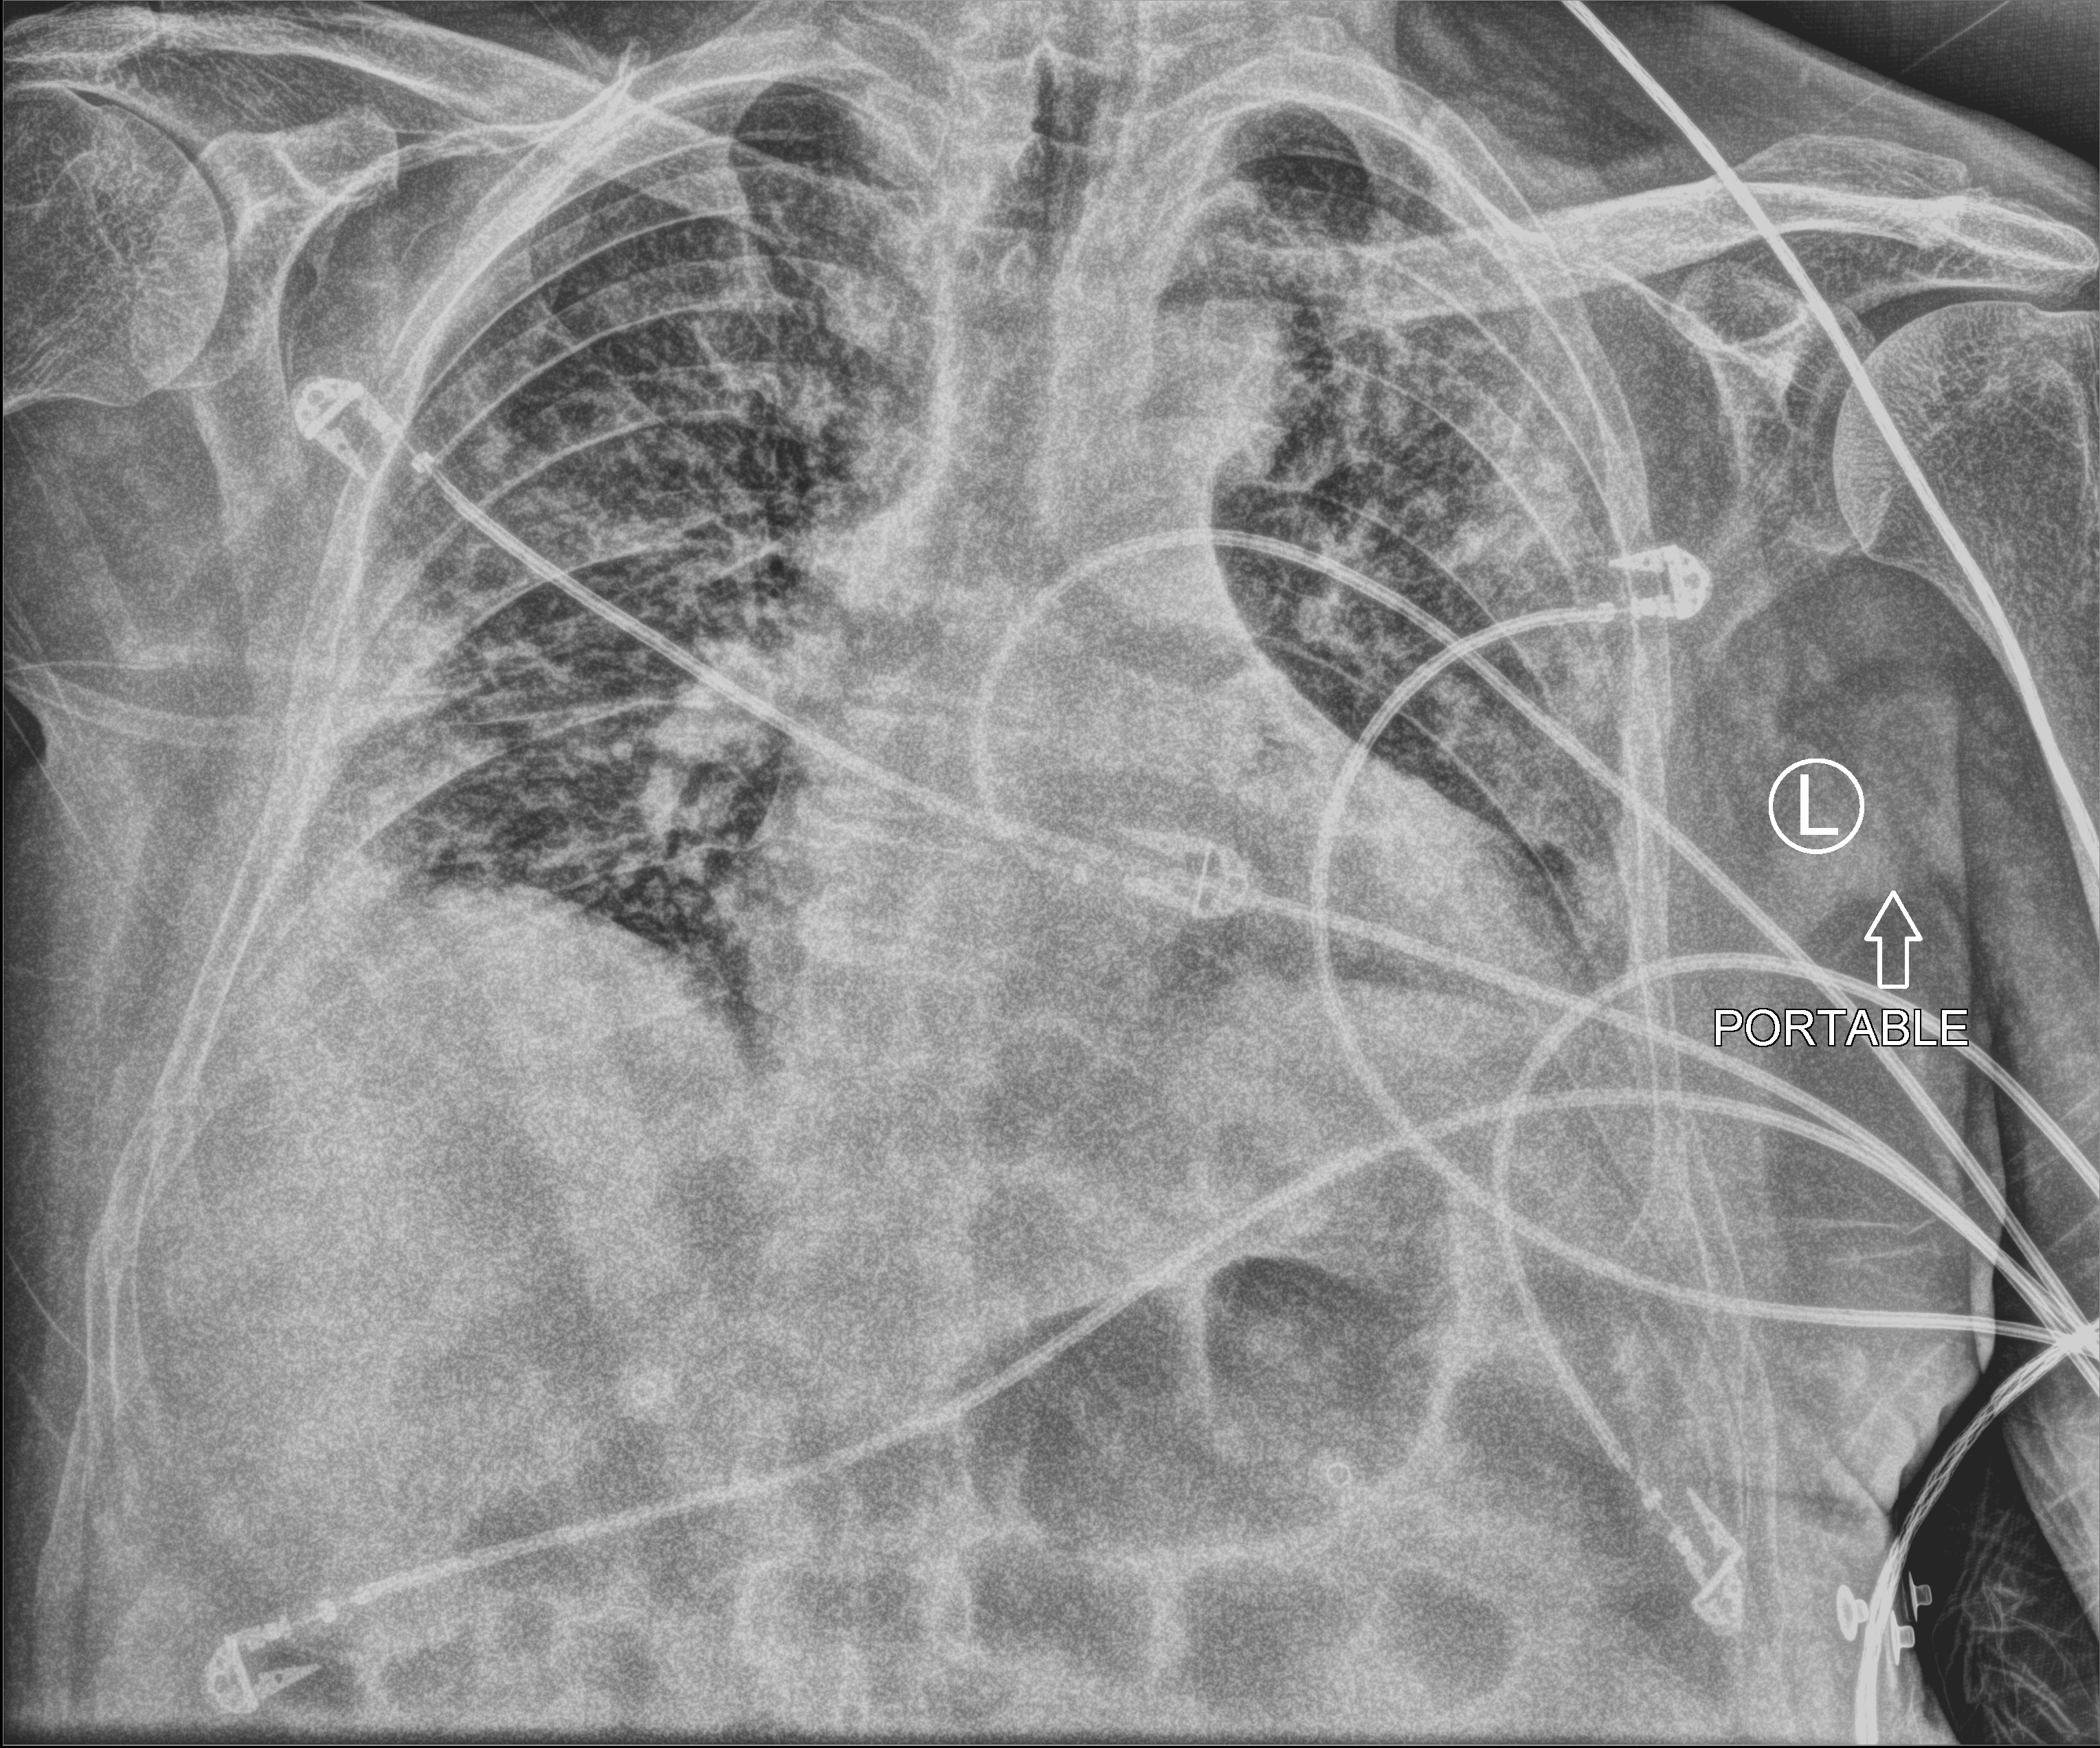
Portable chest radiograph, anteroposterior (AP) projection. Patient hospitalised with COVID-19; male, aged 60–74 years.
Hospital-stay facts (about this admission, not read from this image; timing relative to this image not recorded):
- hypertension (admission record): yes
- diabetes (admission record): no
- admitted to intensive care during this hospital stay: no